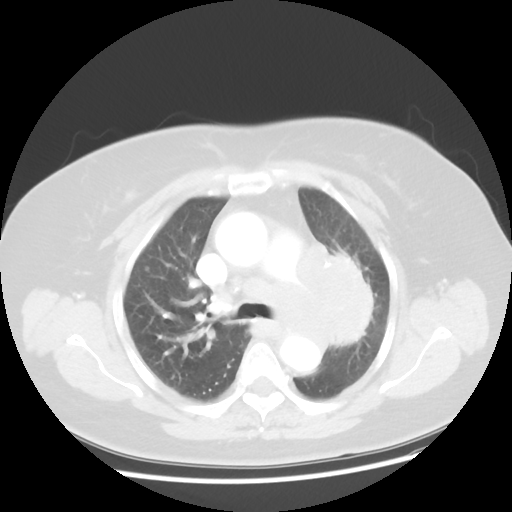
Chest CT, one axial slice. Position 31 of 49 along the scan axis. Reconstruction kernel STANDARD. 120 kVp. Lung window (W 1500 / L -600 HU). 512 × 512 image matrix, field of view 374 × 374 mm. Patient: female, 58 years. From the clinical record (not read from this slice): clinical TNM (as recorded): T4 N3 M0; histopathological grade: G3.
Outlined on this slice (bounding box drawn by a radiologist):
- lung tumour (recorded histology: small cell carcinoma): box from (x=267, y=226) to (x=372, y=365) px